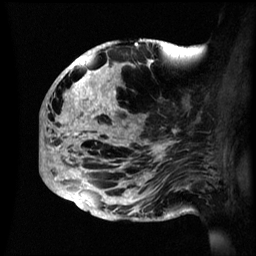
Breast MRI (dynamic contrast-enhanced), one sagittal slice. Slice 27 of 60 in the series (ordered by position). Dynamic contrast-enhanced series, image 2 of 3 at this slice position (ordered by acquisition). 1.5 T. TE 4.2 ms, TR 8.4 ms. 2.4 mm slice thickness. 256 × 256 image matrix, field of view 230 × 230 mm. Patient: female, 48 years.
Annotated regions visible in this slice (semi-automatically segmented with operator editing):
- analysis volume of interest (the breast-tissue region the enhancement analysis was run in; not a lesion): bounding box (x1, y1, x2, y2) in pixels: (41, 41, 195, 221)
- tumour enhancement mask (voxels above the 70 % enhancement threshold inside the analysis volume of interest): (41, 41, 177, 219)